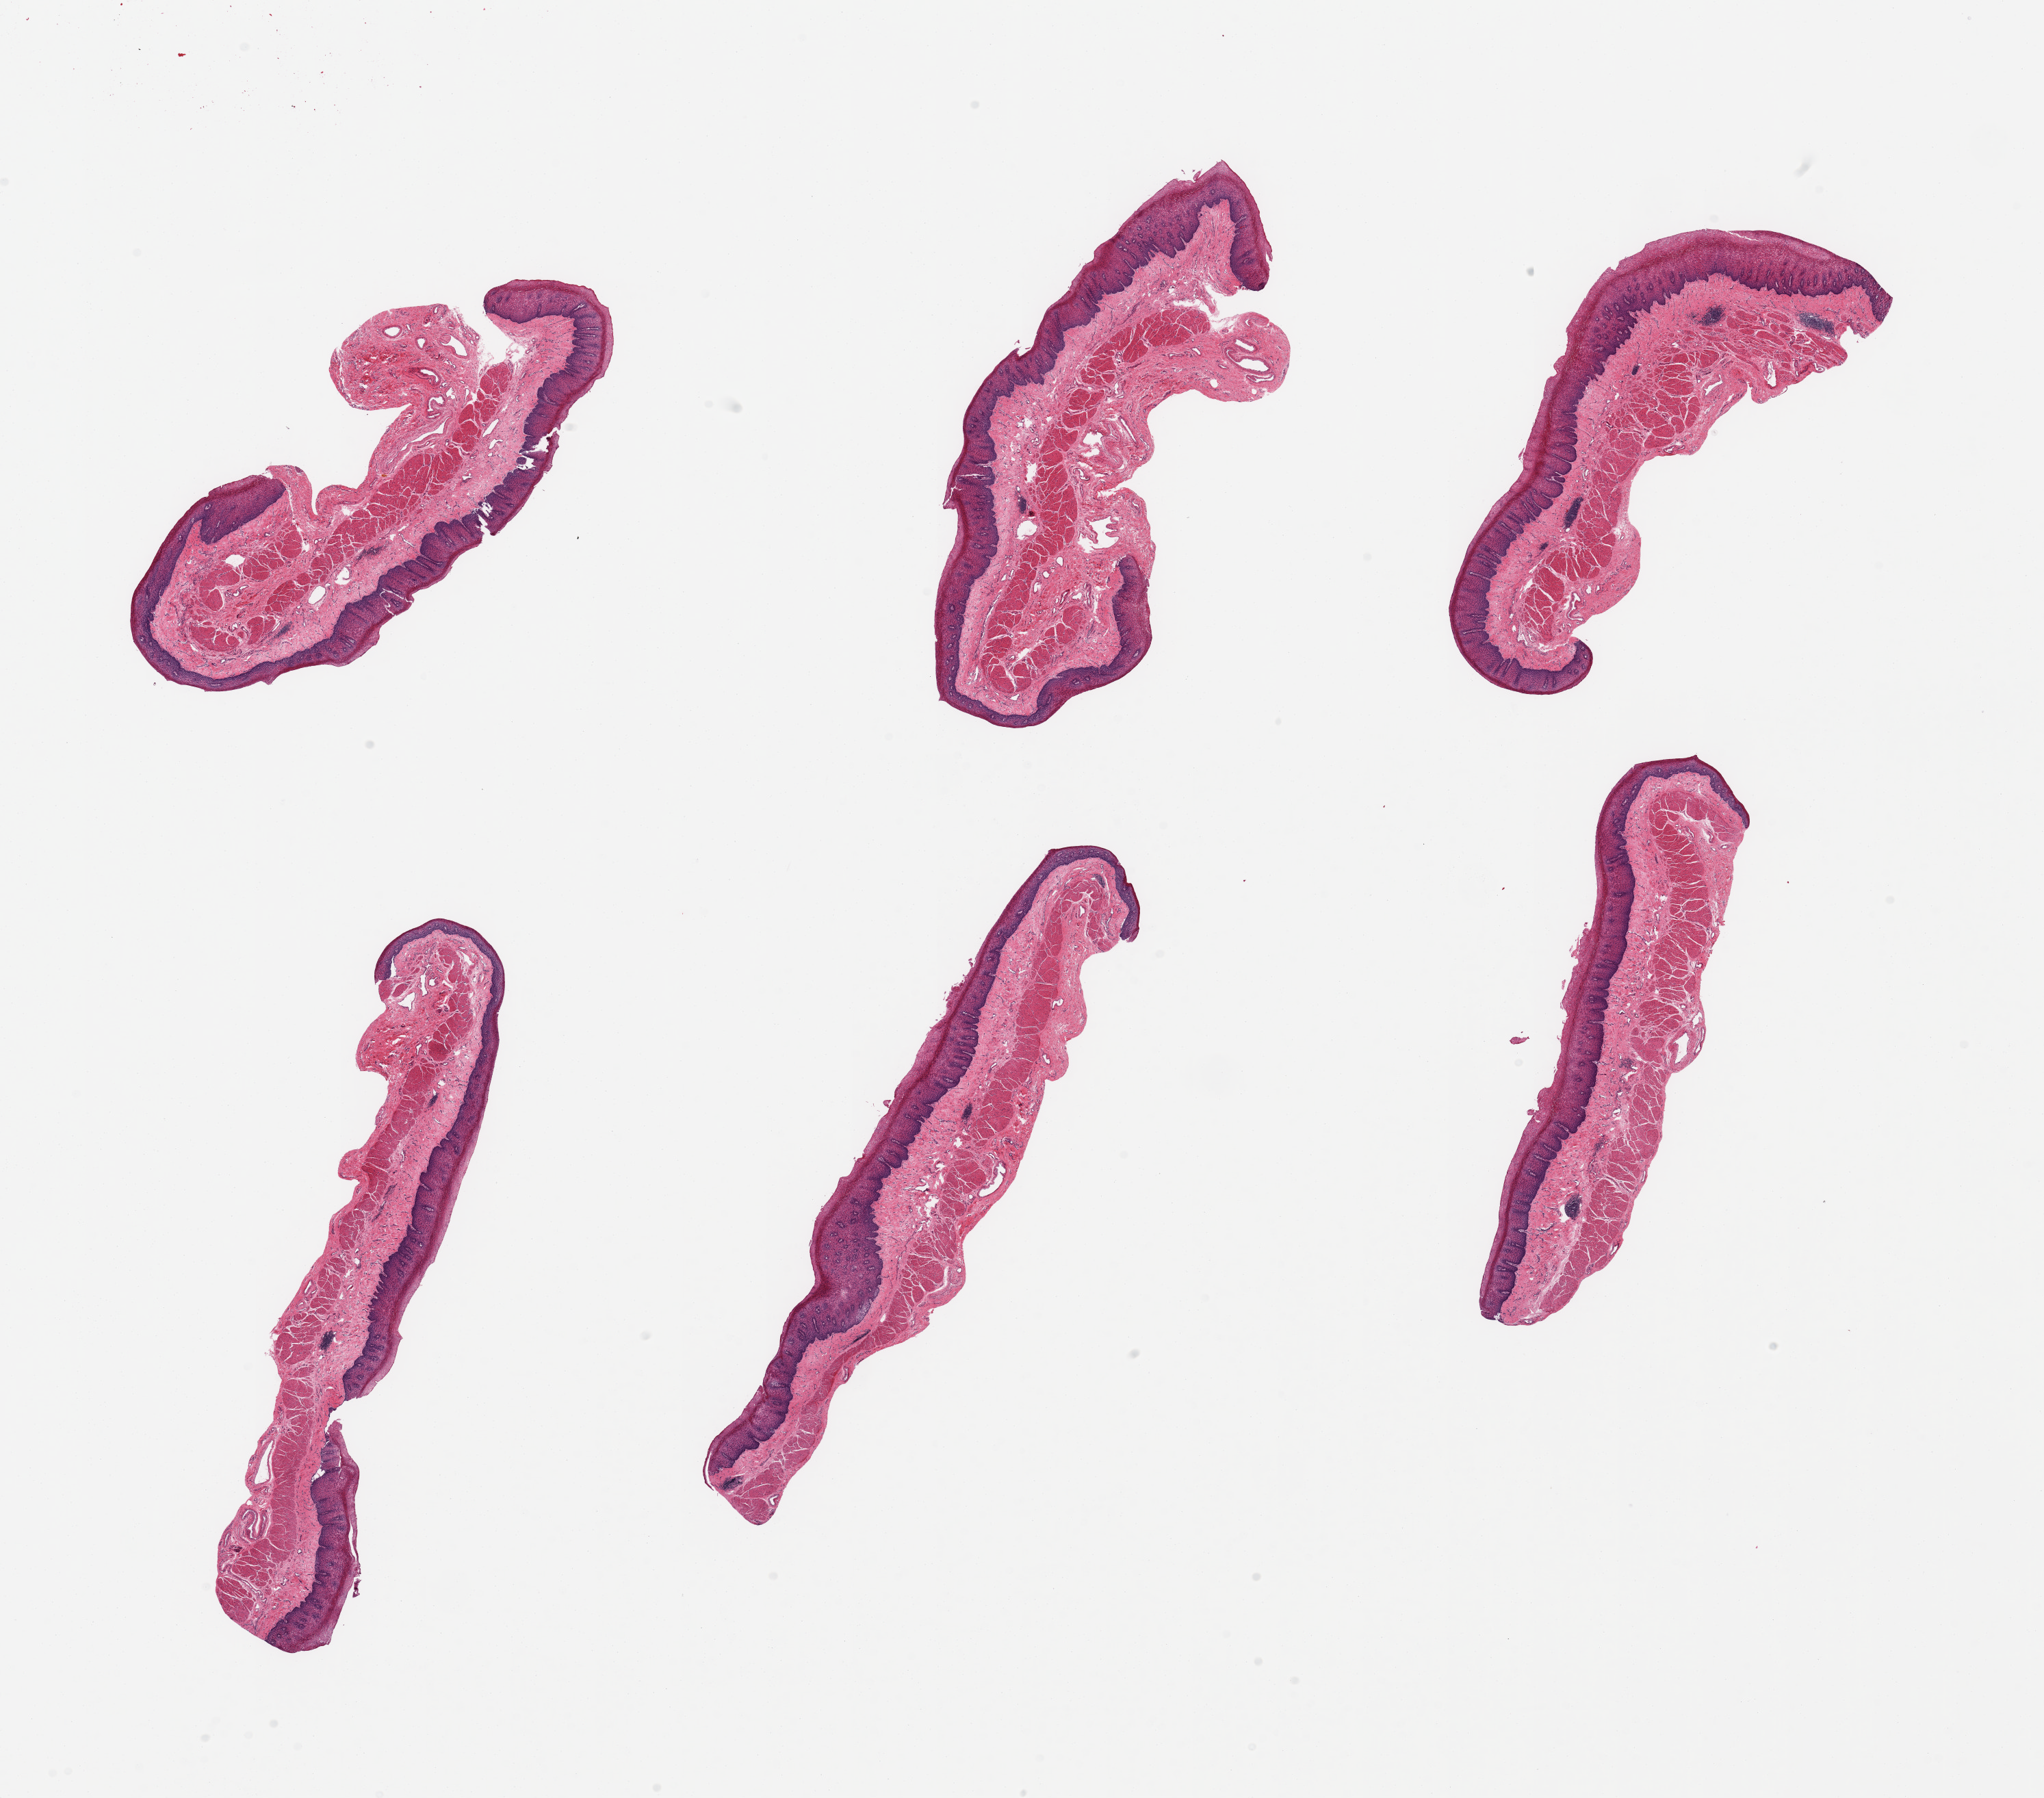
Digitized haematoxylin and eosin-stained section — low-resolution overview of the scanned area, about 23.6 x 20.8 mm (from a 20x scan); PAXgene-fixed paraffin-embedded (PFPE) section; section of esophageal mucous membrane (target tissue); donor tissue sample. Female donor.
Reviewer comment on this tissue sample: 6 pieces; mild to modereate squamous hyperplasia with parakeratosis.